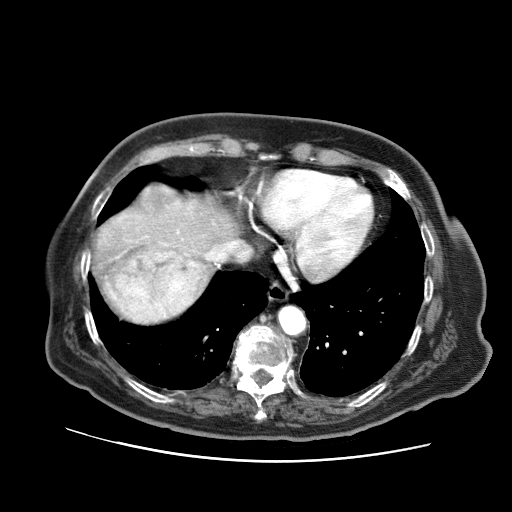
Contrast-enhanced abdominal CT (liver protocol), one axial slice. Slice 60 of 73 in the series (ordered by position). Reconstruction kernel STANDARD. Soft-tissue window (W 400 / L 40 HU). 512 × 512 image matrix. From the clinical record (not read from this slice): diagnosis: hepatocellular carcinoma (patient treated with transarterial chemoembolisation; whether this scan precedes or follows treatment is not stated here); TNM stage (as recorded): Stage-I; Child-Pugh class: A; tumour differentiation: well differentiated; tumour nodularity: uninodular.
Outlined on this slice (semi-automatically segmented with operator editing):
- abdominal aorta: bounding box (x1, y1, x2, y2) in pixels: (280, 306, 305, 334)
- liver parenchyma outside the tumour (the mass and vessels are separate outlines, so this box may not span the whole liver): (90, 185, 236, 316)
- mass: (107, 247, 207, 324)
- liver vessels: (164, 230, 216, 260)